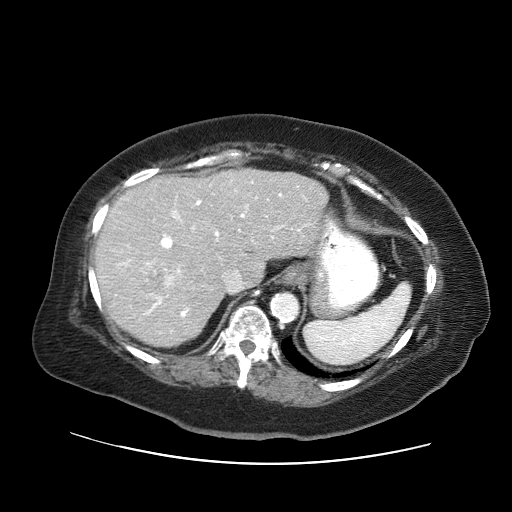
Contrast-enhanced abdominal CT (liver protocol), one axial slice; slice 42 of 71 in the series (ordered by position); 120 kVp; soft-tissue window (W 400 / L 40 HU); 2.5 mm slice thickness; 512 × 512 image matrix. Case-level facts recorded for this patient, not image findings: diagnosis: hepatocellular carcinoma (patient treated with transarterial chemoembolisation; whether this scan precedes or follows treatment is not stated here); TNM stage (as recorded): Stage-II; Child-Pugh class: A; tumour differentiation: poorly differentiated; tumour size: 5 cm.
Outlined on this slice (semi-automatic segmentation, software-assisted and operator-edited):
- liver parenchyma outside the tumour (the mass and vessels are separate outlines, so this box may not span the whole liver): box from (x=94, y=168) to (x=328, y=346) px
- mass: (x=141, y=268)–(x=174, y=295)
- liver vessels: (x=117, y=181)–(x=307, y=333)